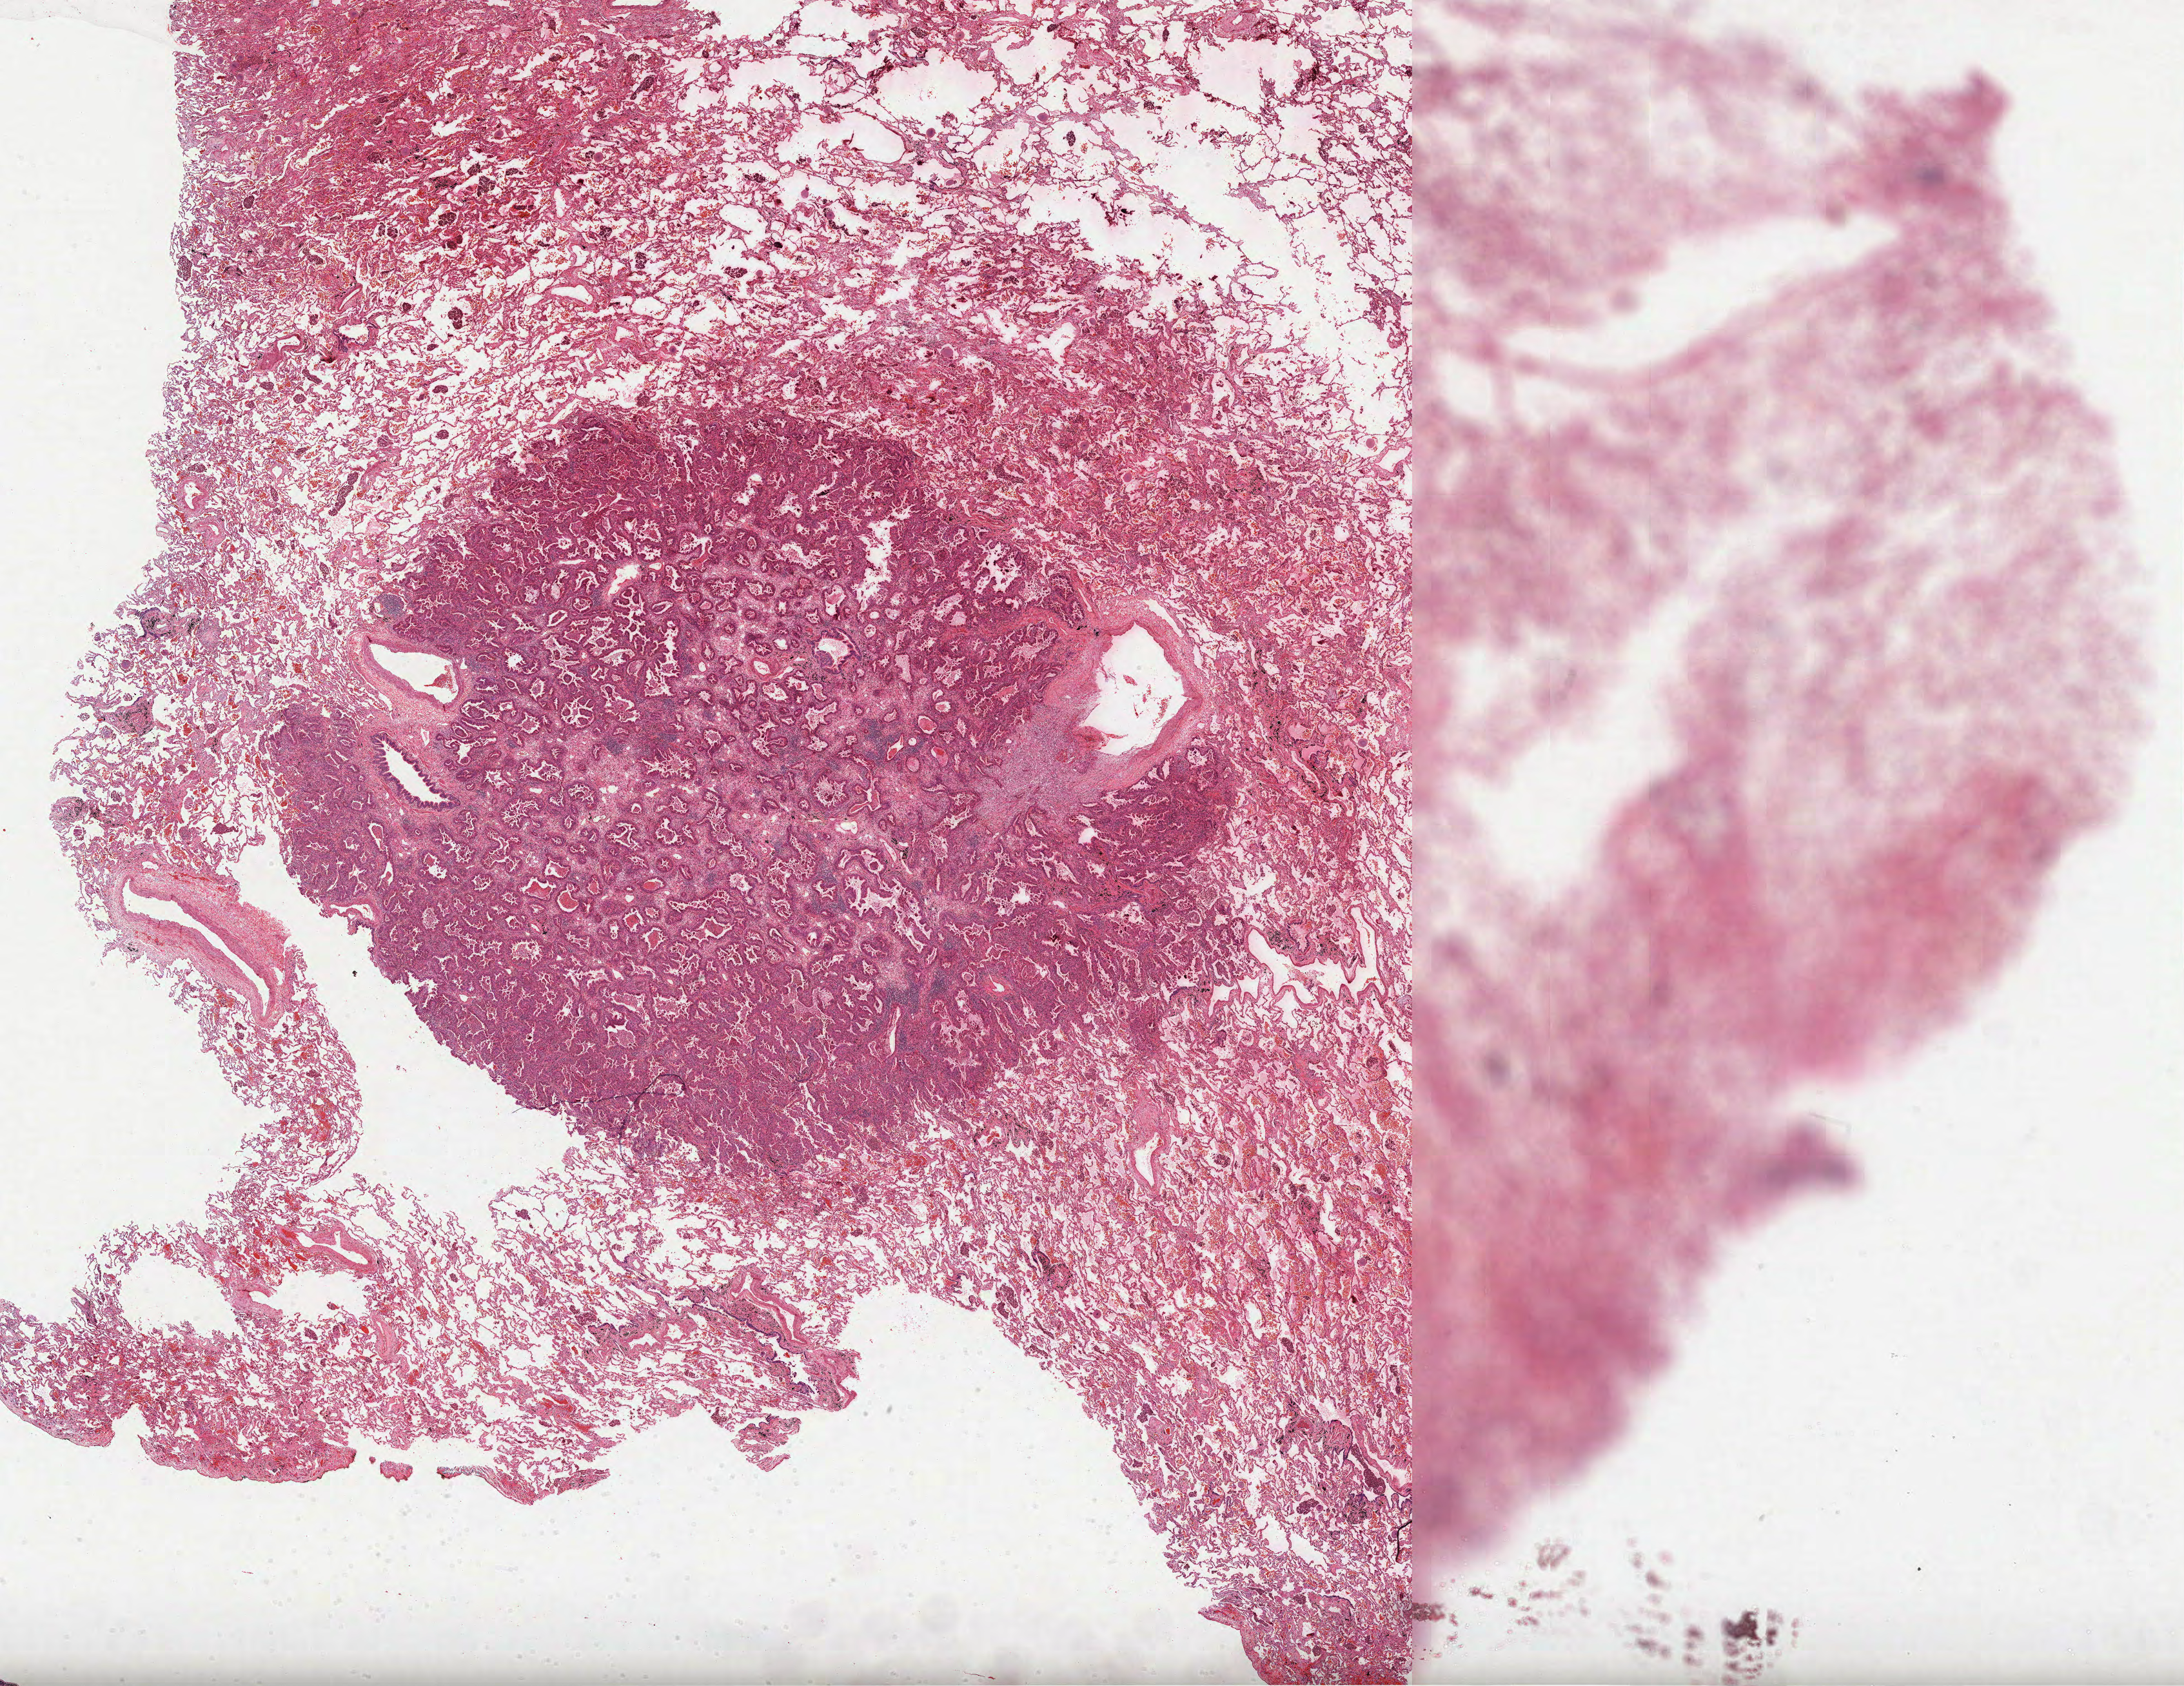
H&E-stained whole-slide image — whole scanned area (about 27.3 x 21.1 mm) shown as a low-resolution overview. FFPE section. Sample: primary tumour, lung. Patient: female, age at initial diagnosis 84 years.
AJCC pathologic stage: I (6th edition). Laterality: right. Diagnosis: Adenocarcinoma, NOS (upper lobe, lung).